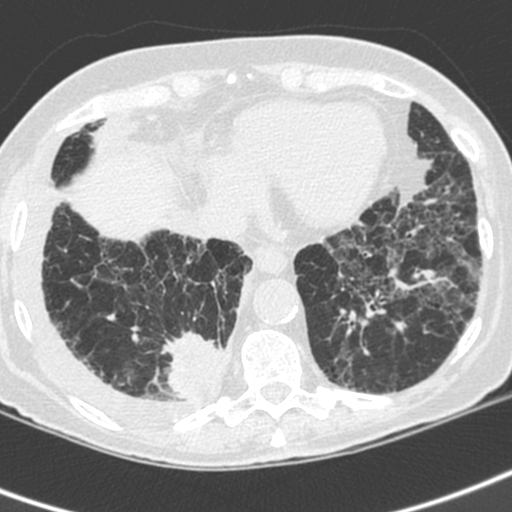
Low-dose screening chest CT, axial slice. First (baseline) screen. Lung window (W 1500 / L -600 HU). Slice 142 of 192 in the series. Female, age 73 years at enrolment. Current smoker at enrolment.
Expert-annotated lung lesion, bounding box (x1, y1, x2, y2) in pixels: (157, 320, 235, 406). Reader record for this screening exam (exam-level; its link to the box is not recorded): non-calcified nodule or mass ≥4 mm, right lower lobe, 35 × 30 mm, spiculated (stellate) margins, soft tissue attenuation. Later outcome: lung cancer diagnosed 22 days after this screen — adenocarcinoma, NOS, right lower lobe, stage IV (AJCC 6th edition), 35 mm at pathology.